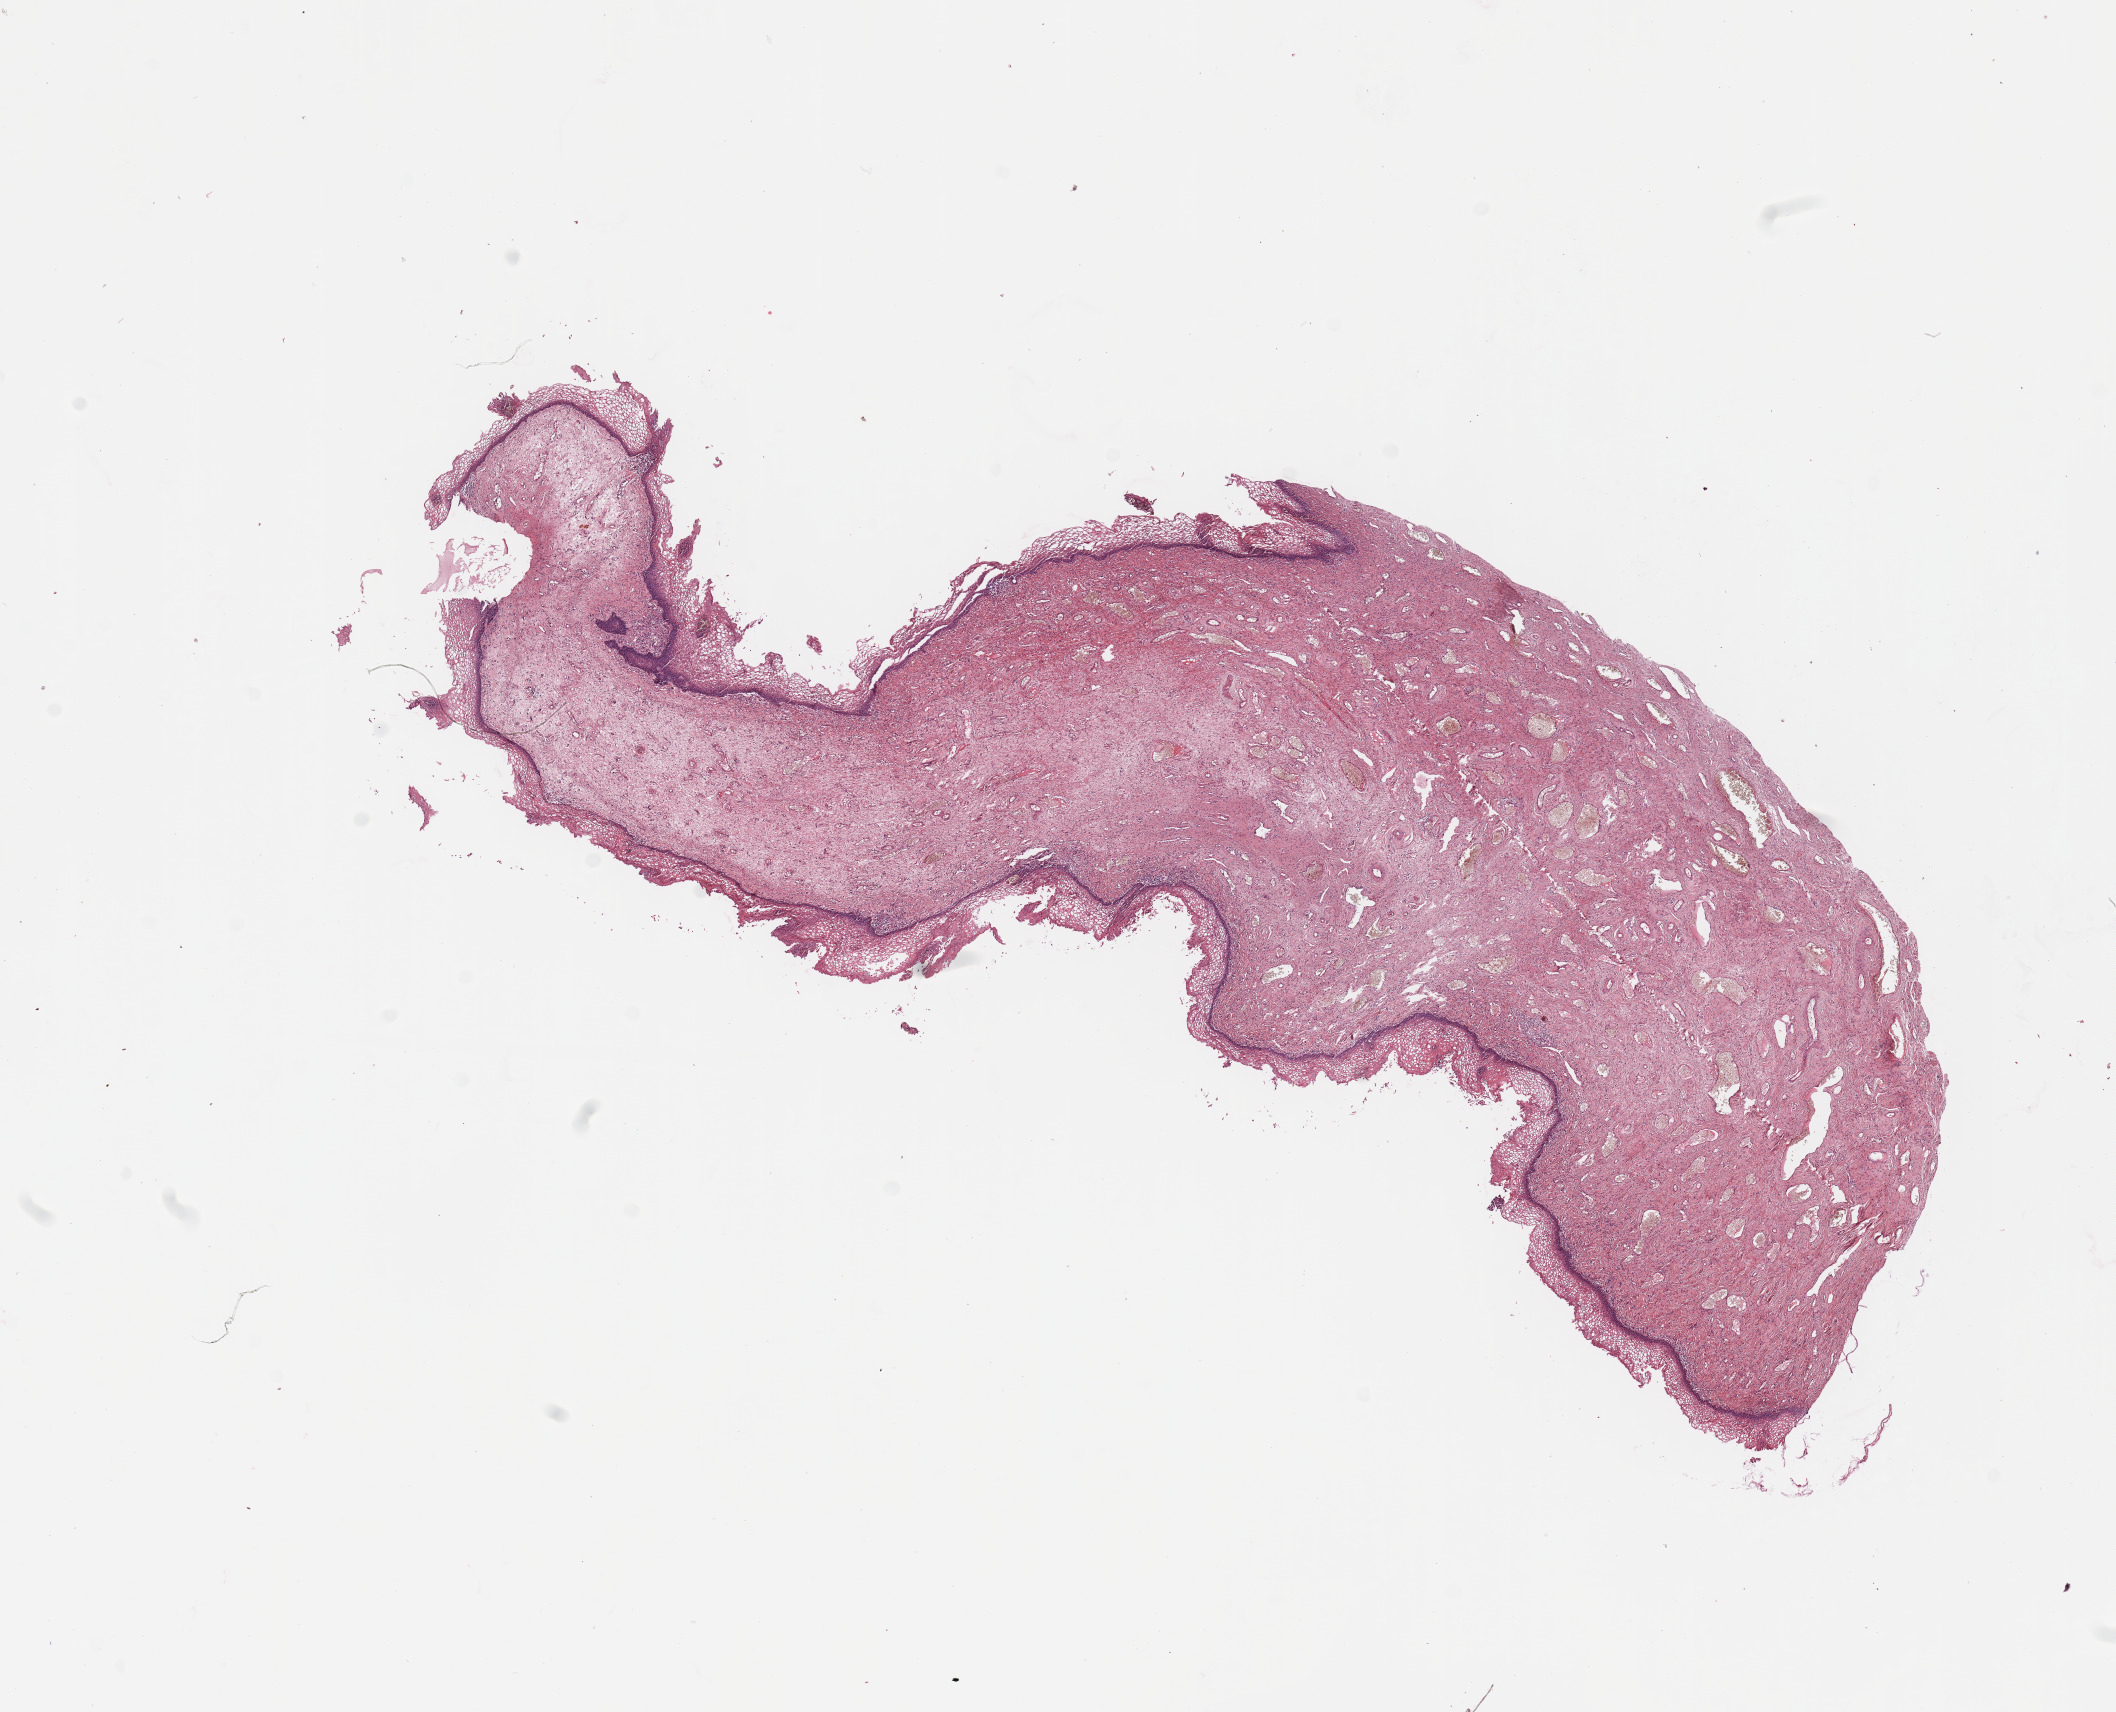
Digitized H&E-stained tissue section (whole slide), a low-resolution overview of the entire scanned area, about 16.7 x 13.5 mm (from a 20x scan), normal (non-tumour) tissue sample, sampled site: uterus. Female, 73 y/o.
This section: normal (non-tumour) tissue from the same patient. Patient diagnosis: Endometrioid adenocarcinoma, NOS.